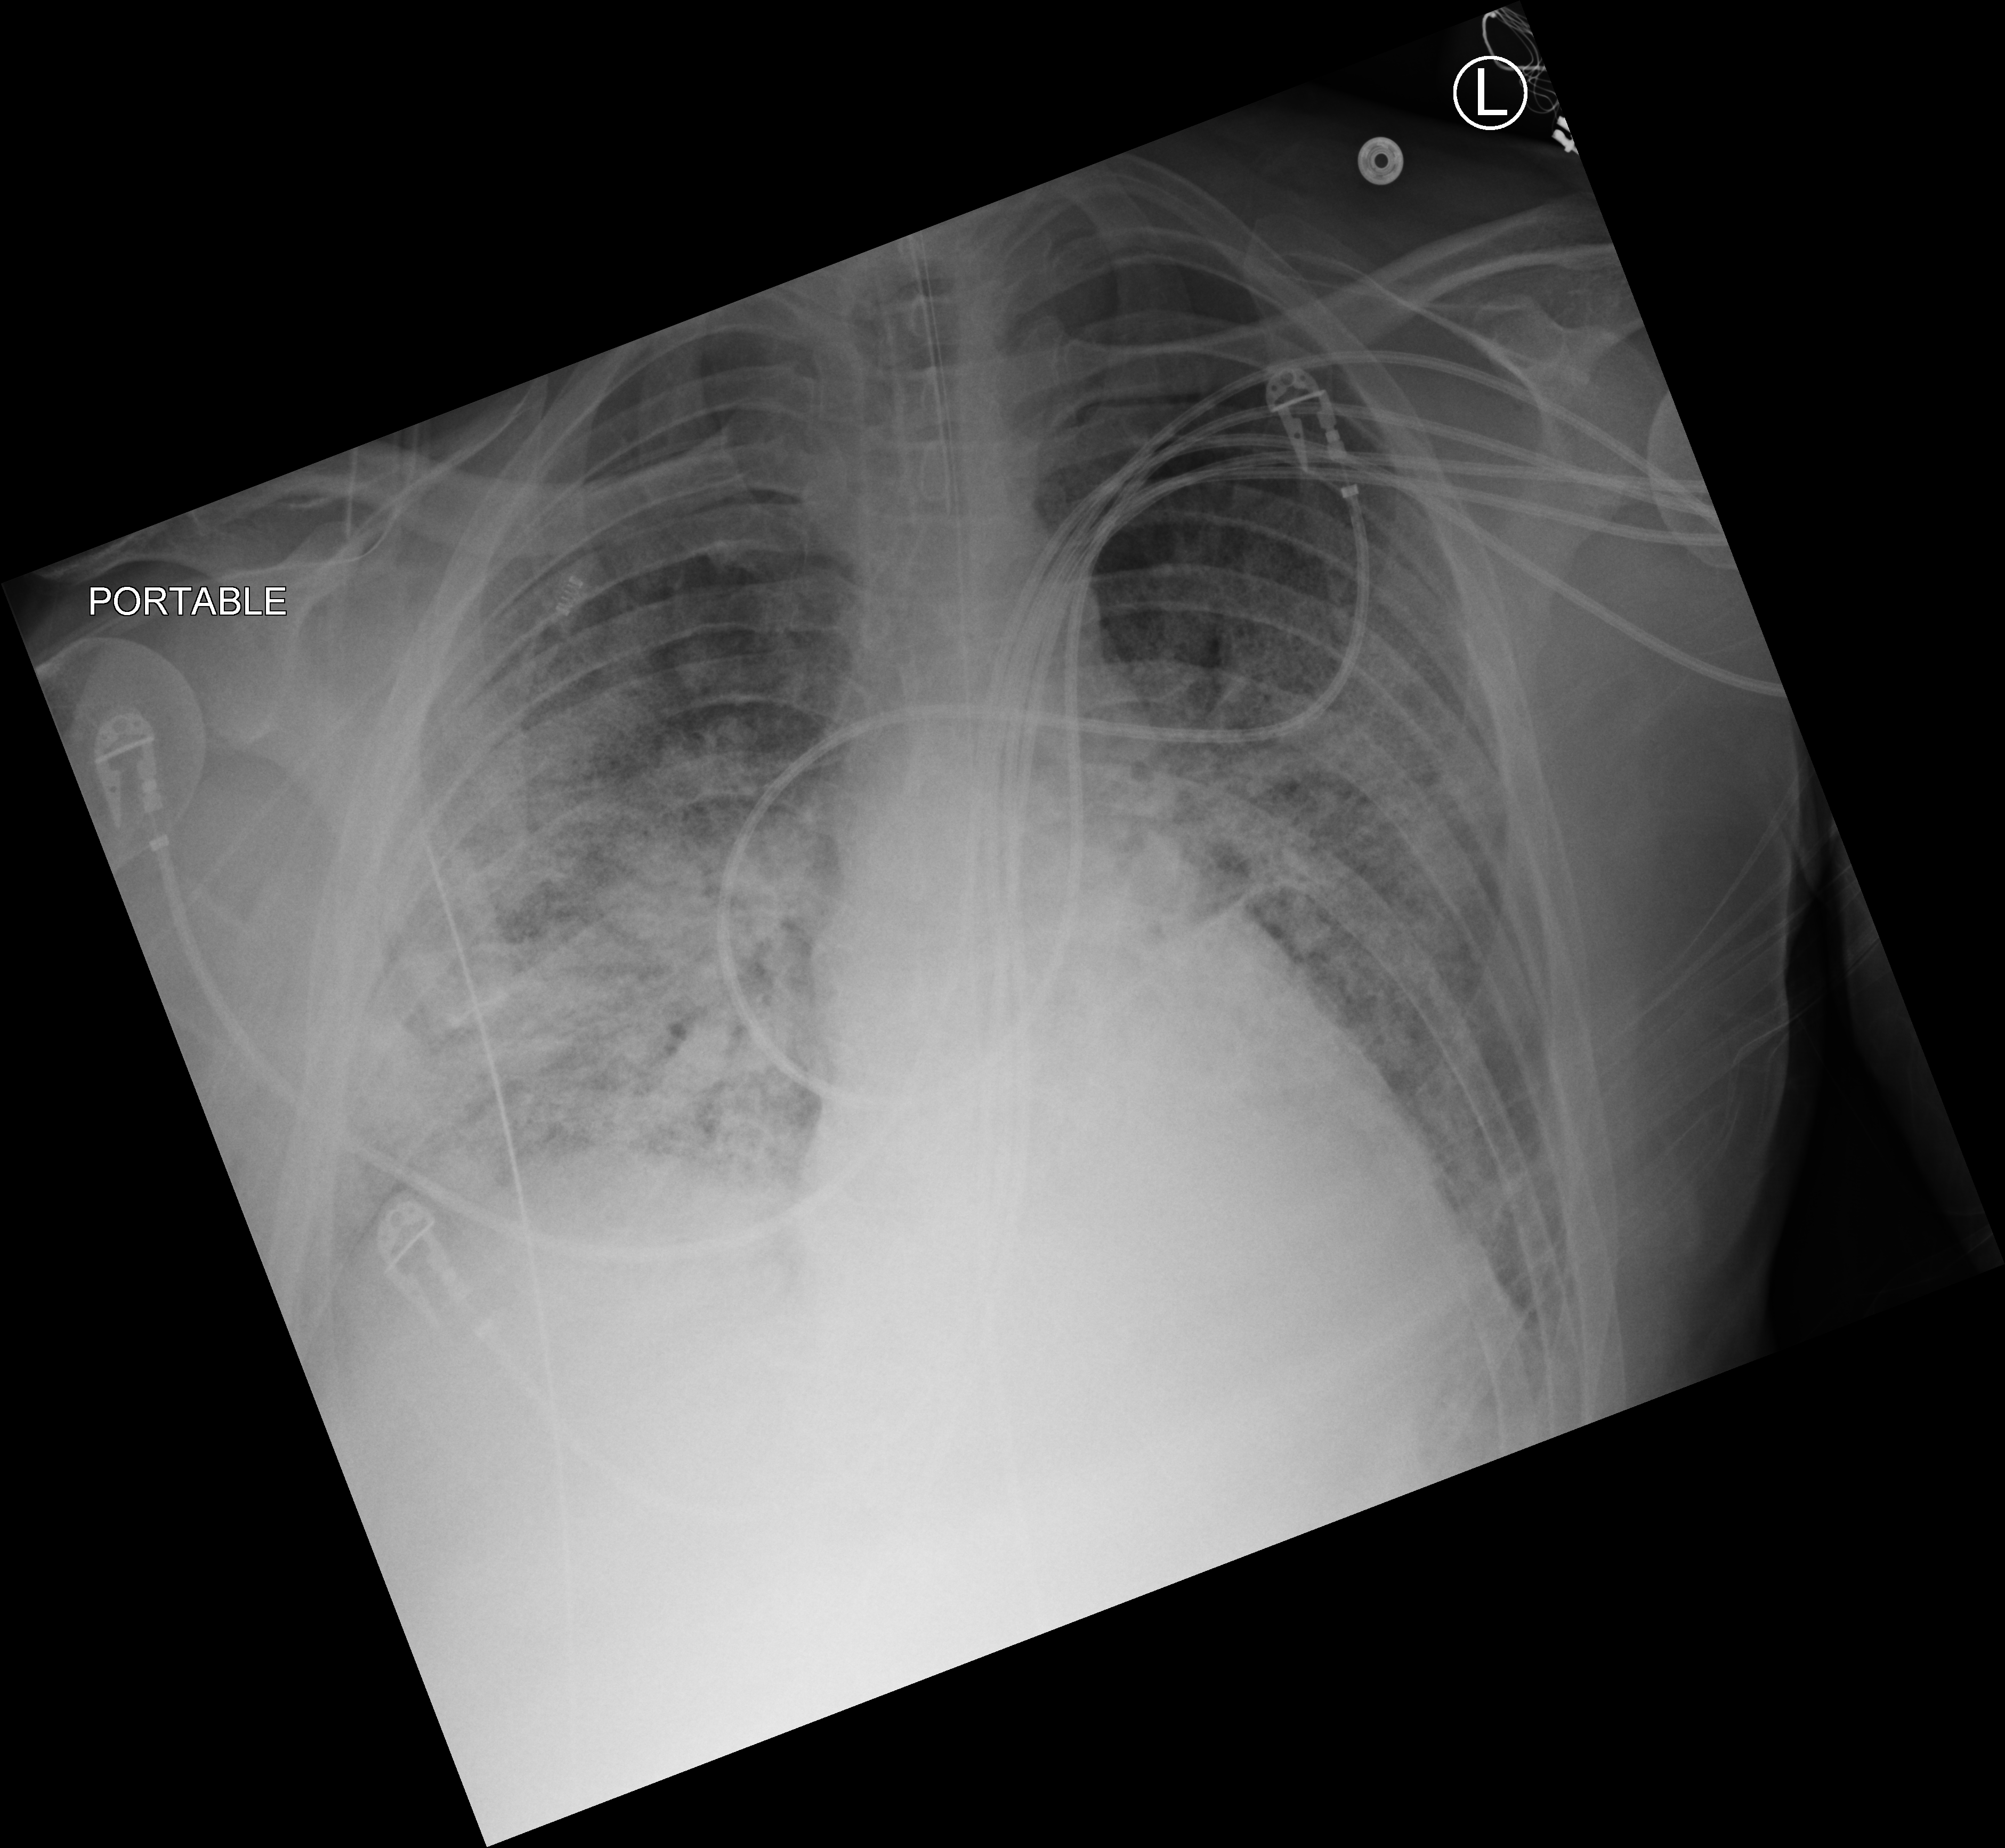
Chest X-ray (portable). Patient hospitalised with COVID-19; male, aged 18–59 years.
Admission-level facts for this patient (not findings on this image; timing relative to this image not recorded): length of hospital stay: 75 days; mechanically ventilated during this hospital stay: yes; admitted to intensive care during this hospital stay: yes.